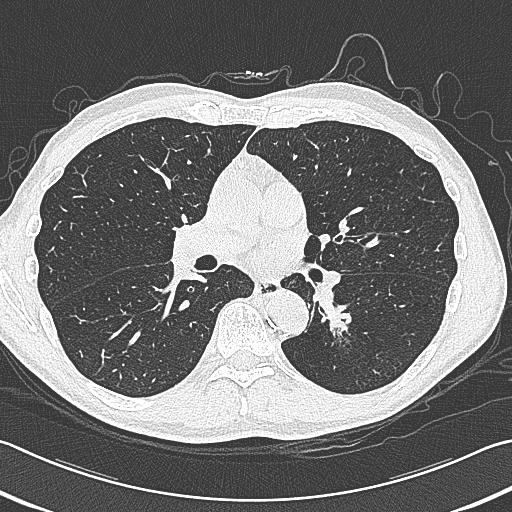
Chest CT (low-dose screening protocol), one axial image. Baseline screening round. Lung window (W 1500 / L -600 HU). 1 mm slice thickness. Lung (sharp) reconstruction kernel (B80f). 512 × 512 image matrix. Male, age 59 years at enrolment.
- Lesion marked by an expert reader, bounding box (x1, y1, x2, y2) in pixels: (314, 293, 375, 353).
- Screening reader's record for this exam (one nodule recorded; not confirmed to be the boxed lesion): non-calcified nodule or mass ≥4 mm, left lower lobe, 15 × 15 mm, smooth margins, soft tissue attenuation.